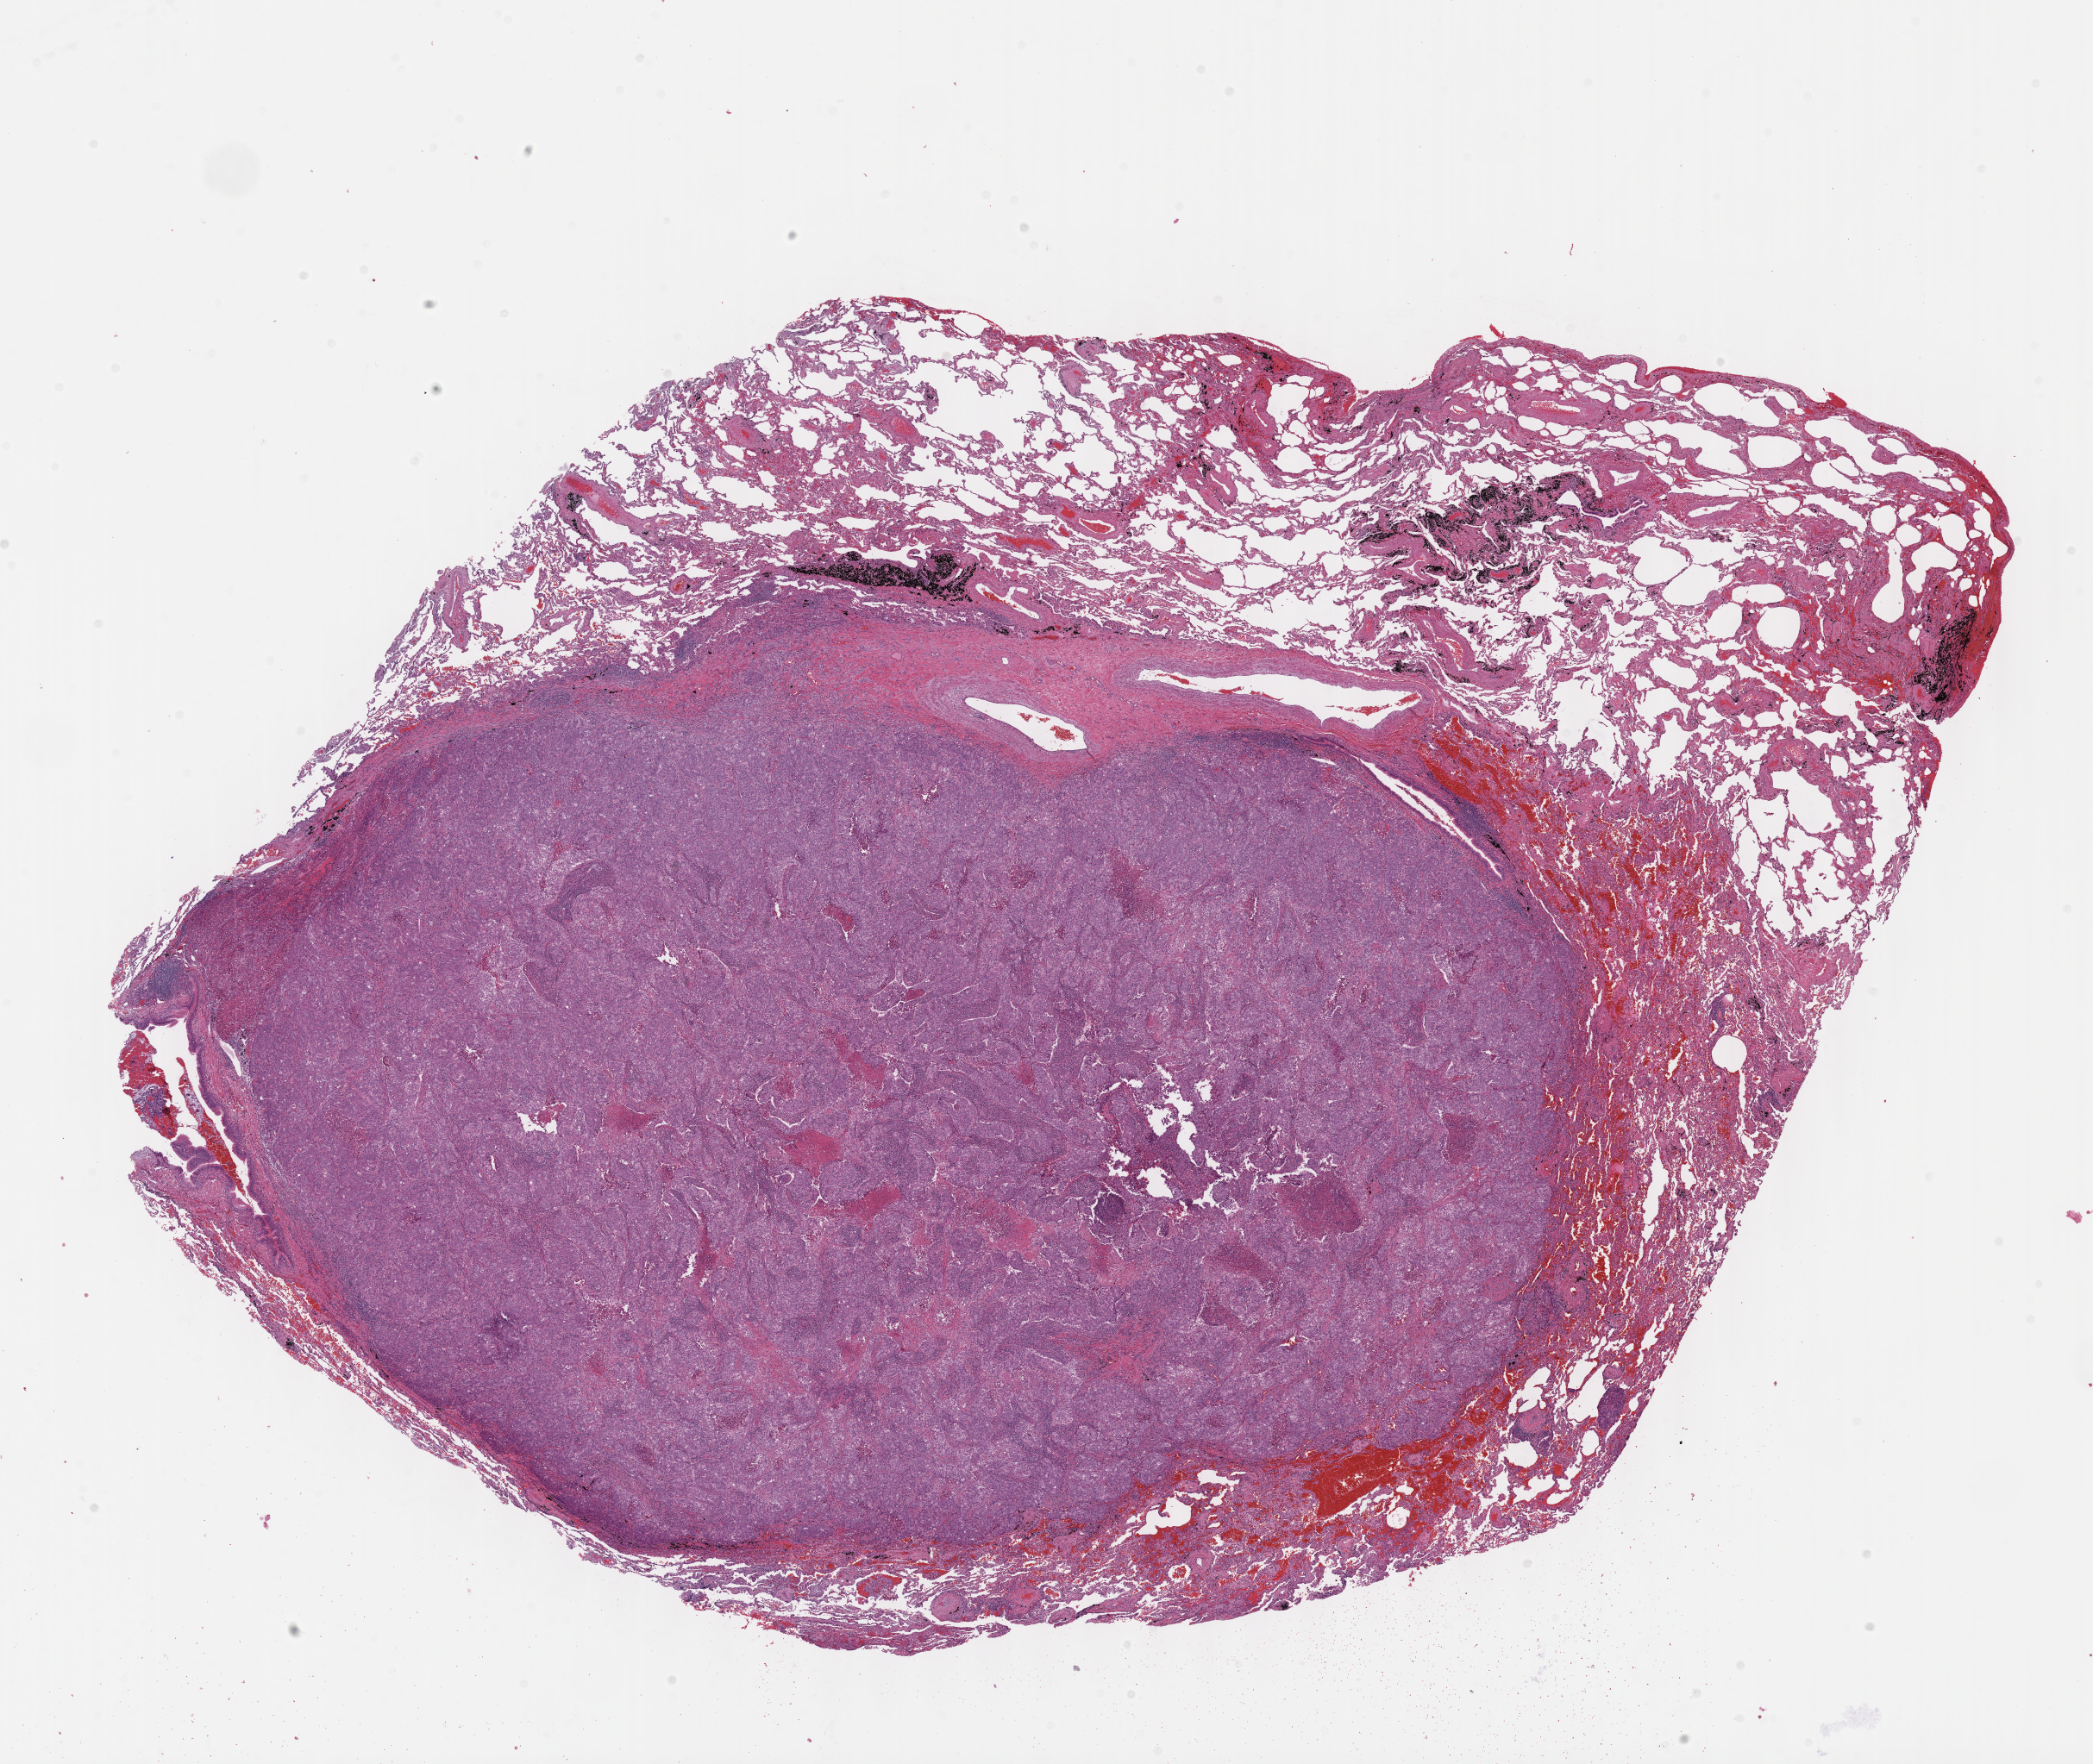
Hematoxylin and eosin (H&E) stained whole-slide image, a low-resolution overview of the entire scanned area, about 19.6 x 16.5 mm; formalin-fixed paraffin-embedded (FFPE) diagnostic section; sample: primary tumour, lung. Male, age 62 years at initial diagnosis.
Histologic diagnosis: Squamous cell carcinoma, NOS.